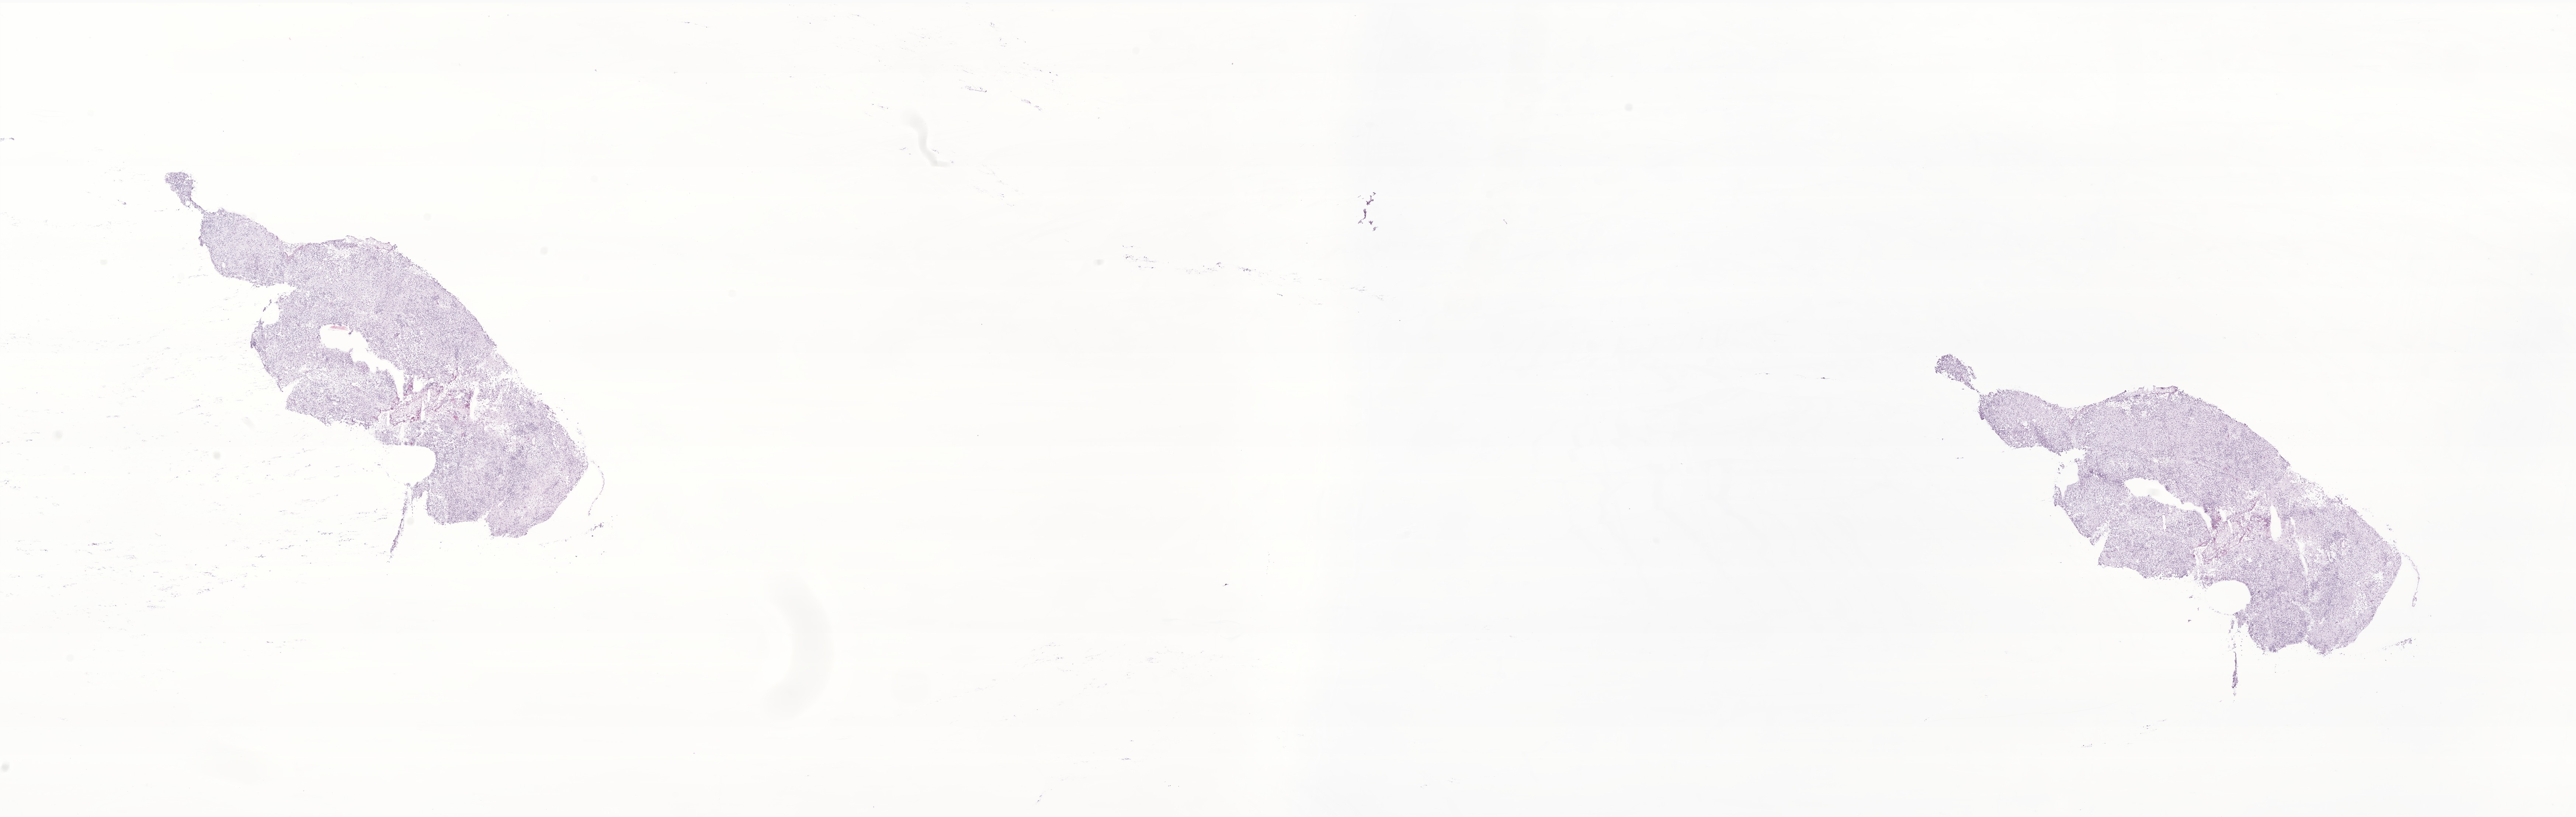
Digitized haematoxylin and eosin-stained section of tumor tissue from the brain — low-resolution overview of the scanned area, about 29.5 x 9.3 mm; cryosection (OCT / tissue freezing medium). Male patient, age 38 months (3 years 2 months).
Recorded diagnosis: Neoplasm, uncertain whether benign or malignant.